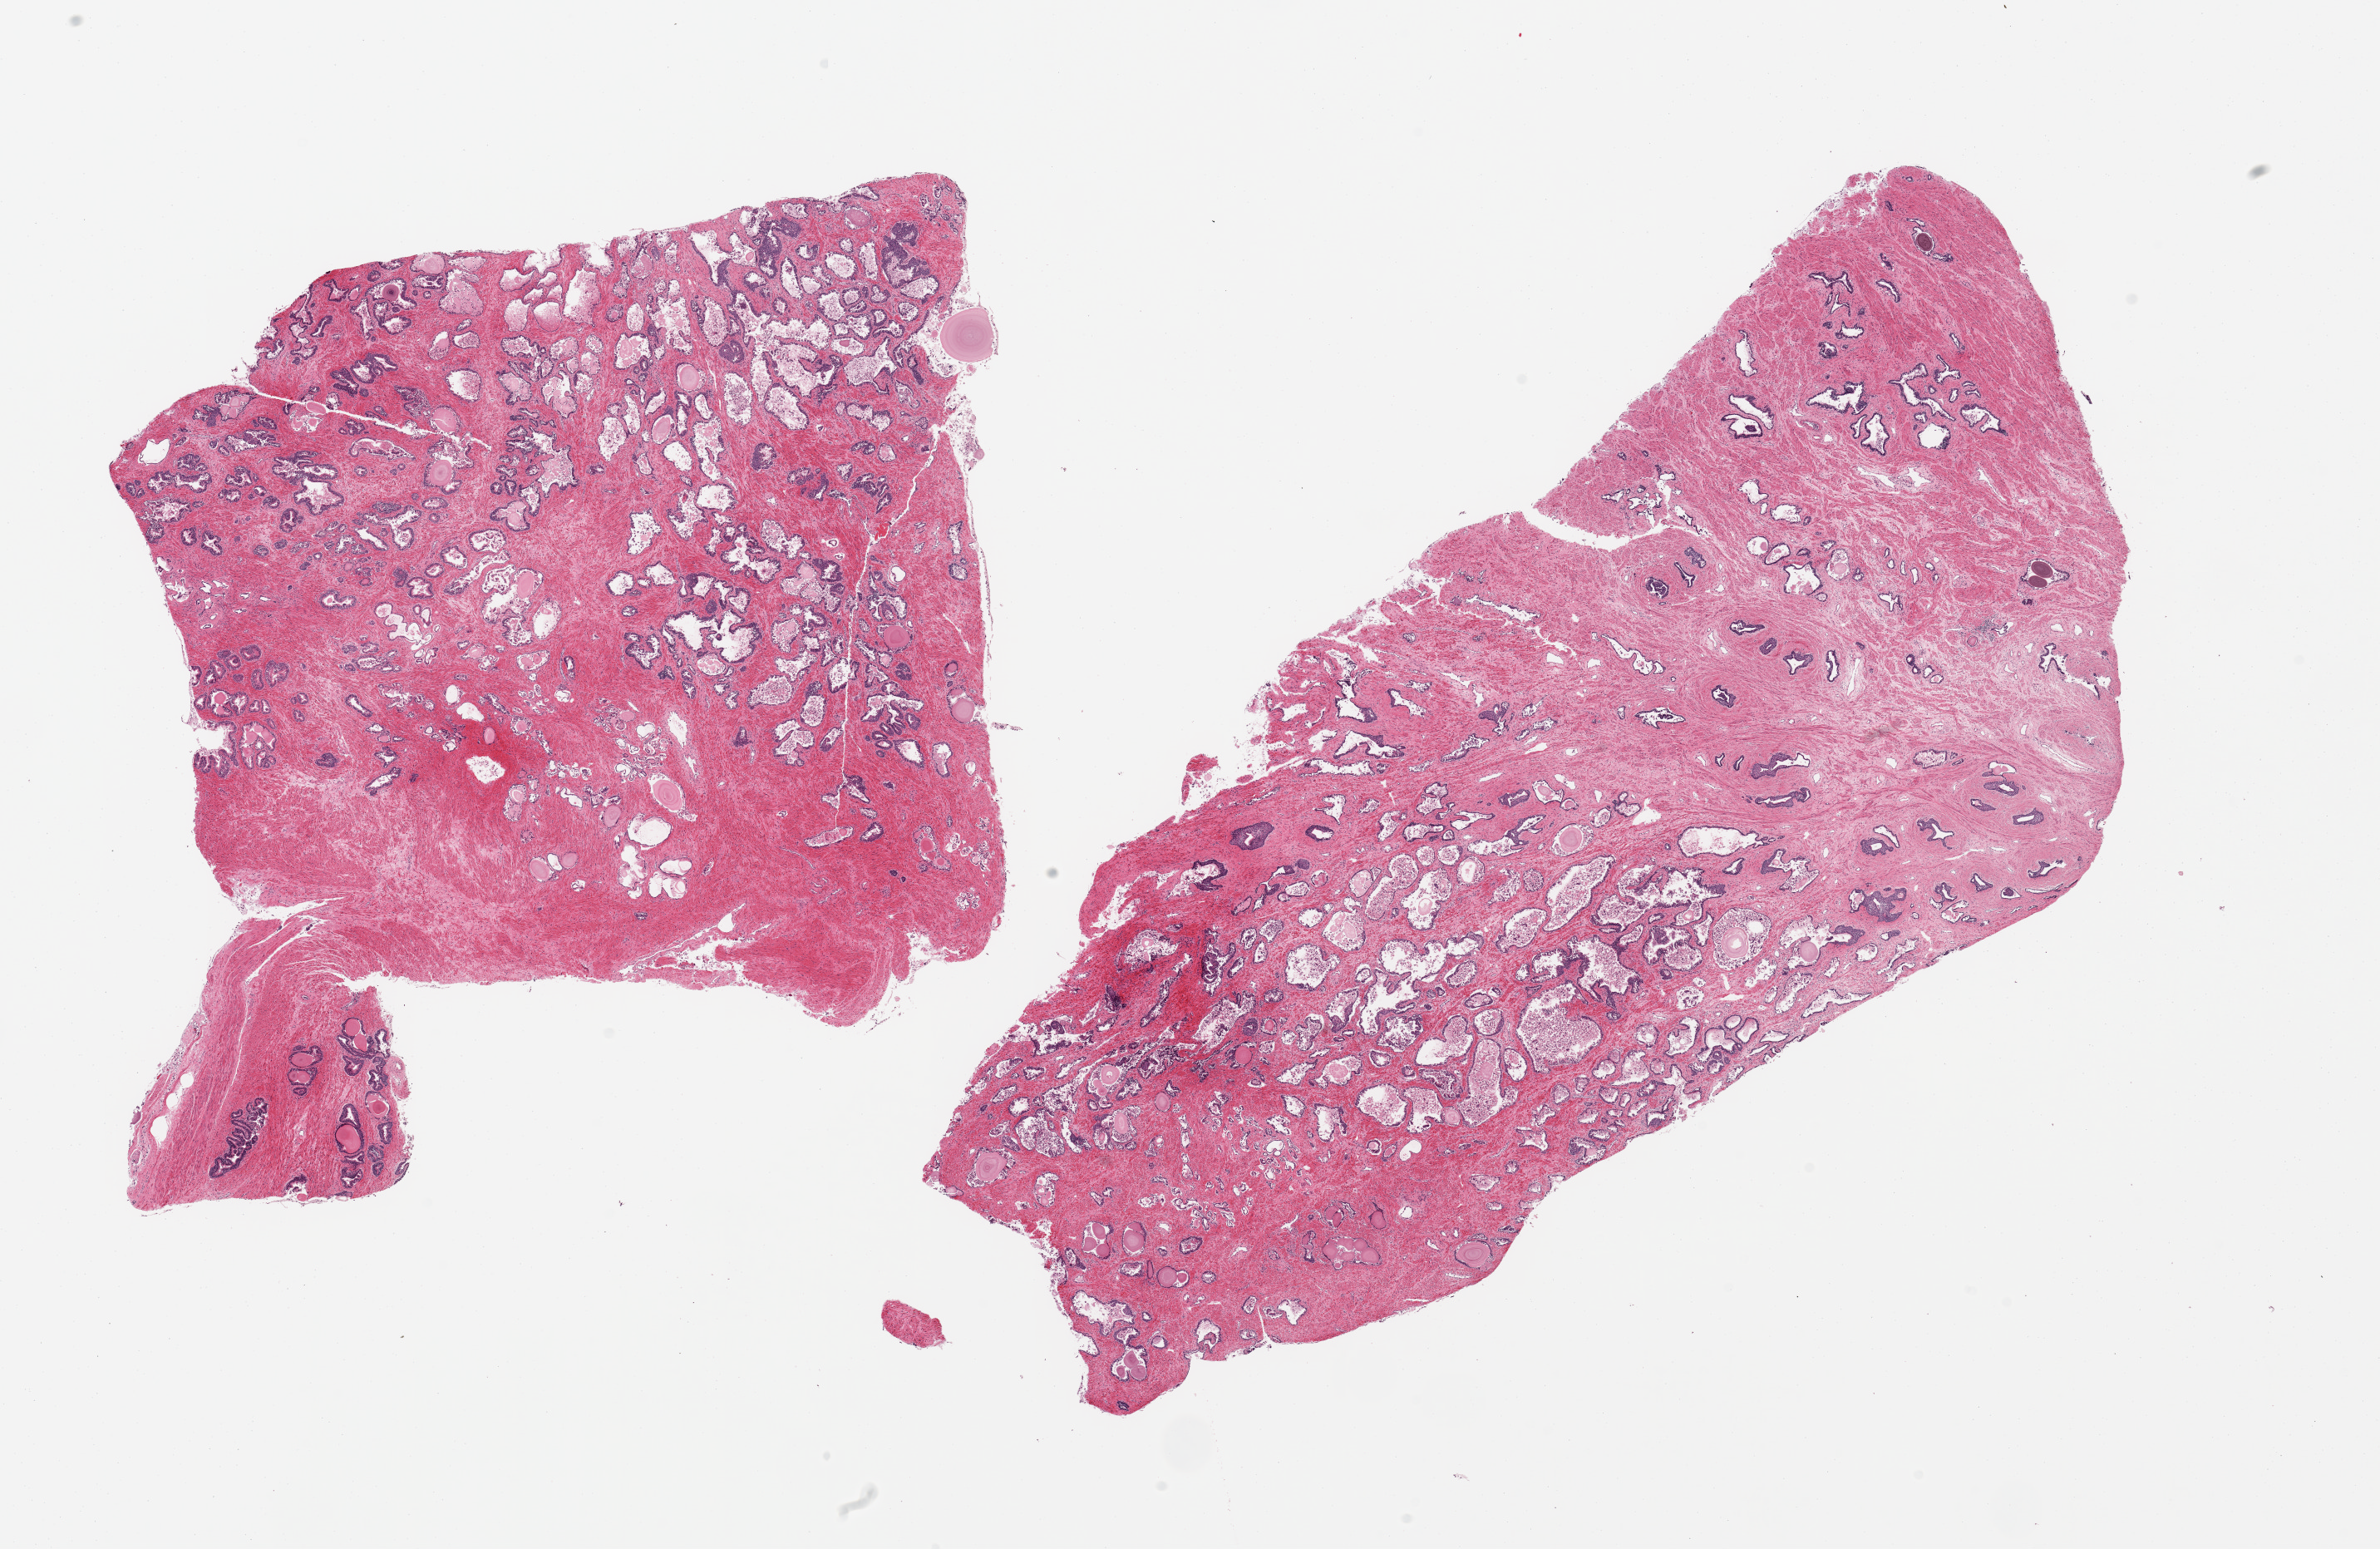
Digitized H&E-stained section, low-resolution overview of the scanned area, about 22.6 x 14.7 mm. PAXgene-fixed paraffin-embedded (PFPE) section. Target tissue: prostate. Donor tissue sample. Male donor.
Pathologist's review note for this sample: 2 pieces.